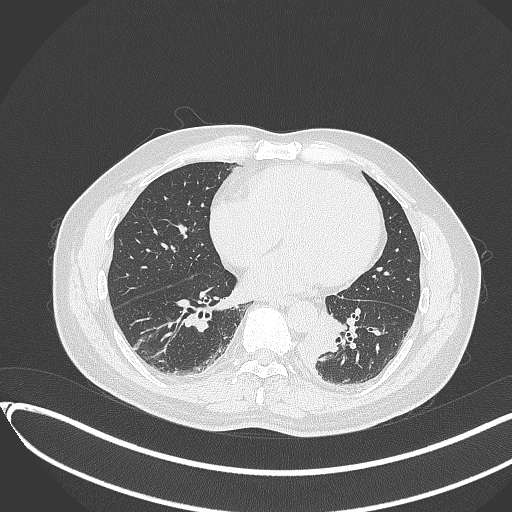
Chest CT, one axial slice; position 127 of 417 along the scan axis; reconstruction kernel B70f; 120 kVp; lung window (W 1500 / L -600 HU); 512 × 512 image matrix, field of view 400 × 400 mm. Patient: male, 54 years. From the clinical record (not read from this slice): clinical TNM (as recorded): T3 N0 M0.
Structures marked on this image (bounding box drawn by a radiologist):
- lung tumour (recorded histology: squamous cell carcinoma): bounding box <298,313,344,368> (left, top, right, bottom; pixels)